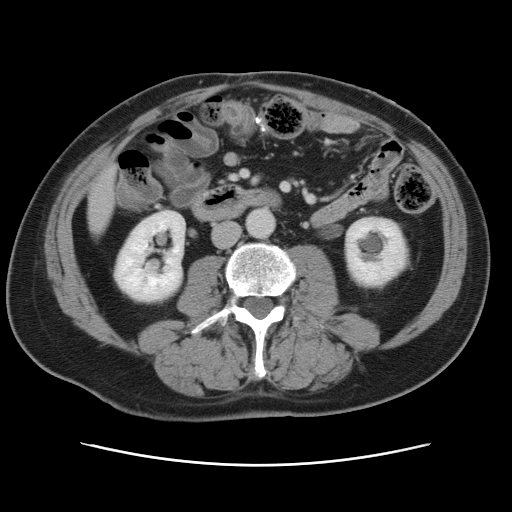
Contrast-enhanced abdominal CT, one axial slice; slice 14 of 80 in the series (ordered by position); 120 kVp; intravenous contrast given; soft-tissue window (W 400 / L 40 HU); 5 mm slice thickness; 512 × 512 image matrix, field of view 370 × 370 mm. Male patient, age 69 years. Case-level facts recorded for this patient, not image findings: diagnosis: colorectal cancer liver metastases, imaged before liver resection; multiple liver metastases: no; largest metastasis: 5 cm; disease in both lobes: yes.
Outlined on this slice (manually delineated by an expert):
- liver: bounding box [x1, y1, x2, y2] px = [88, 170, 115, 229]